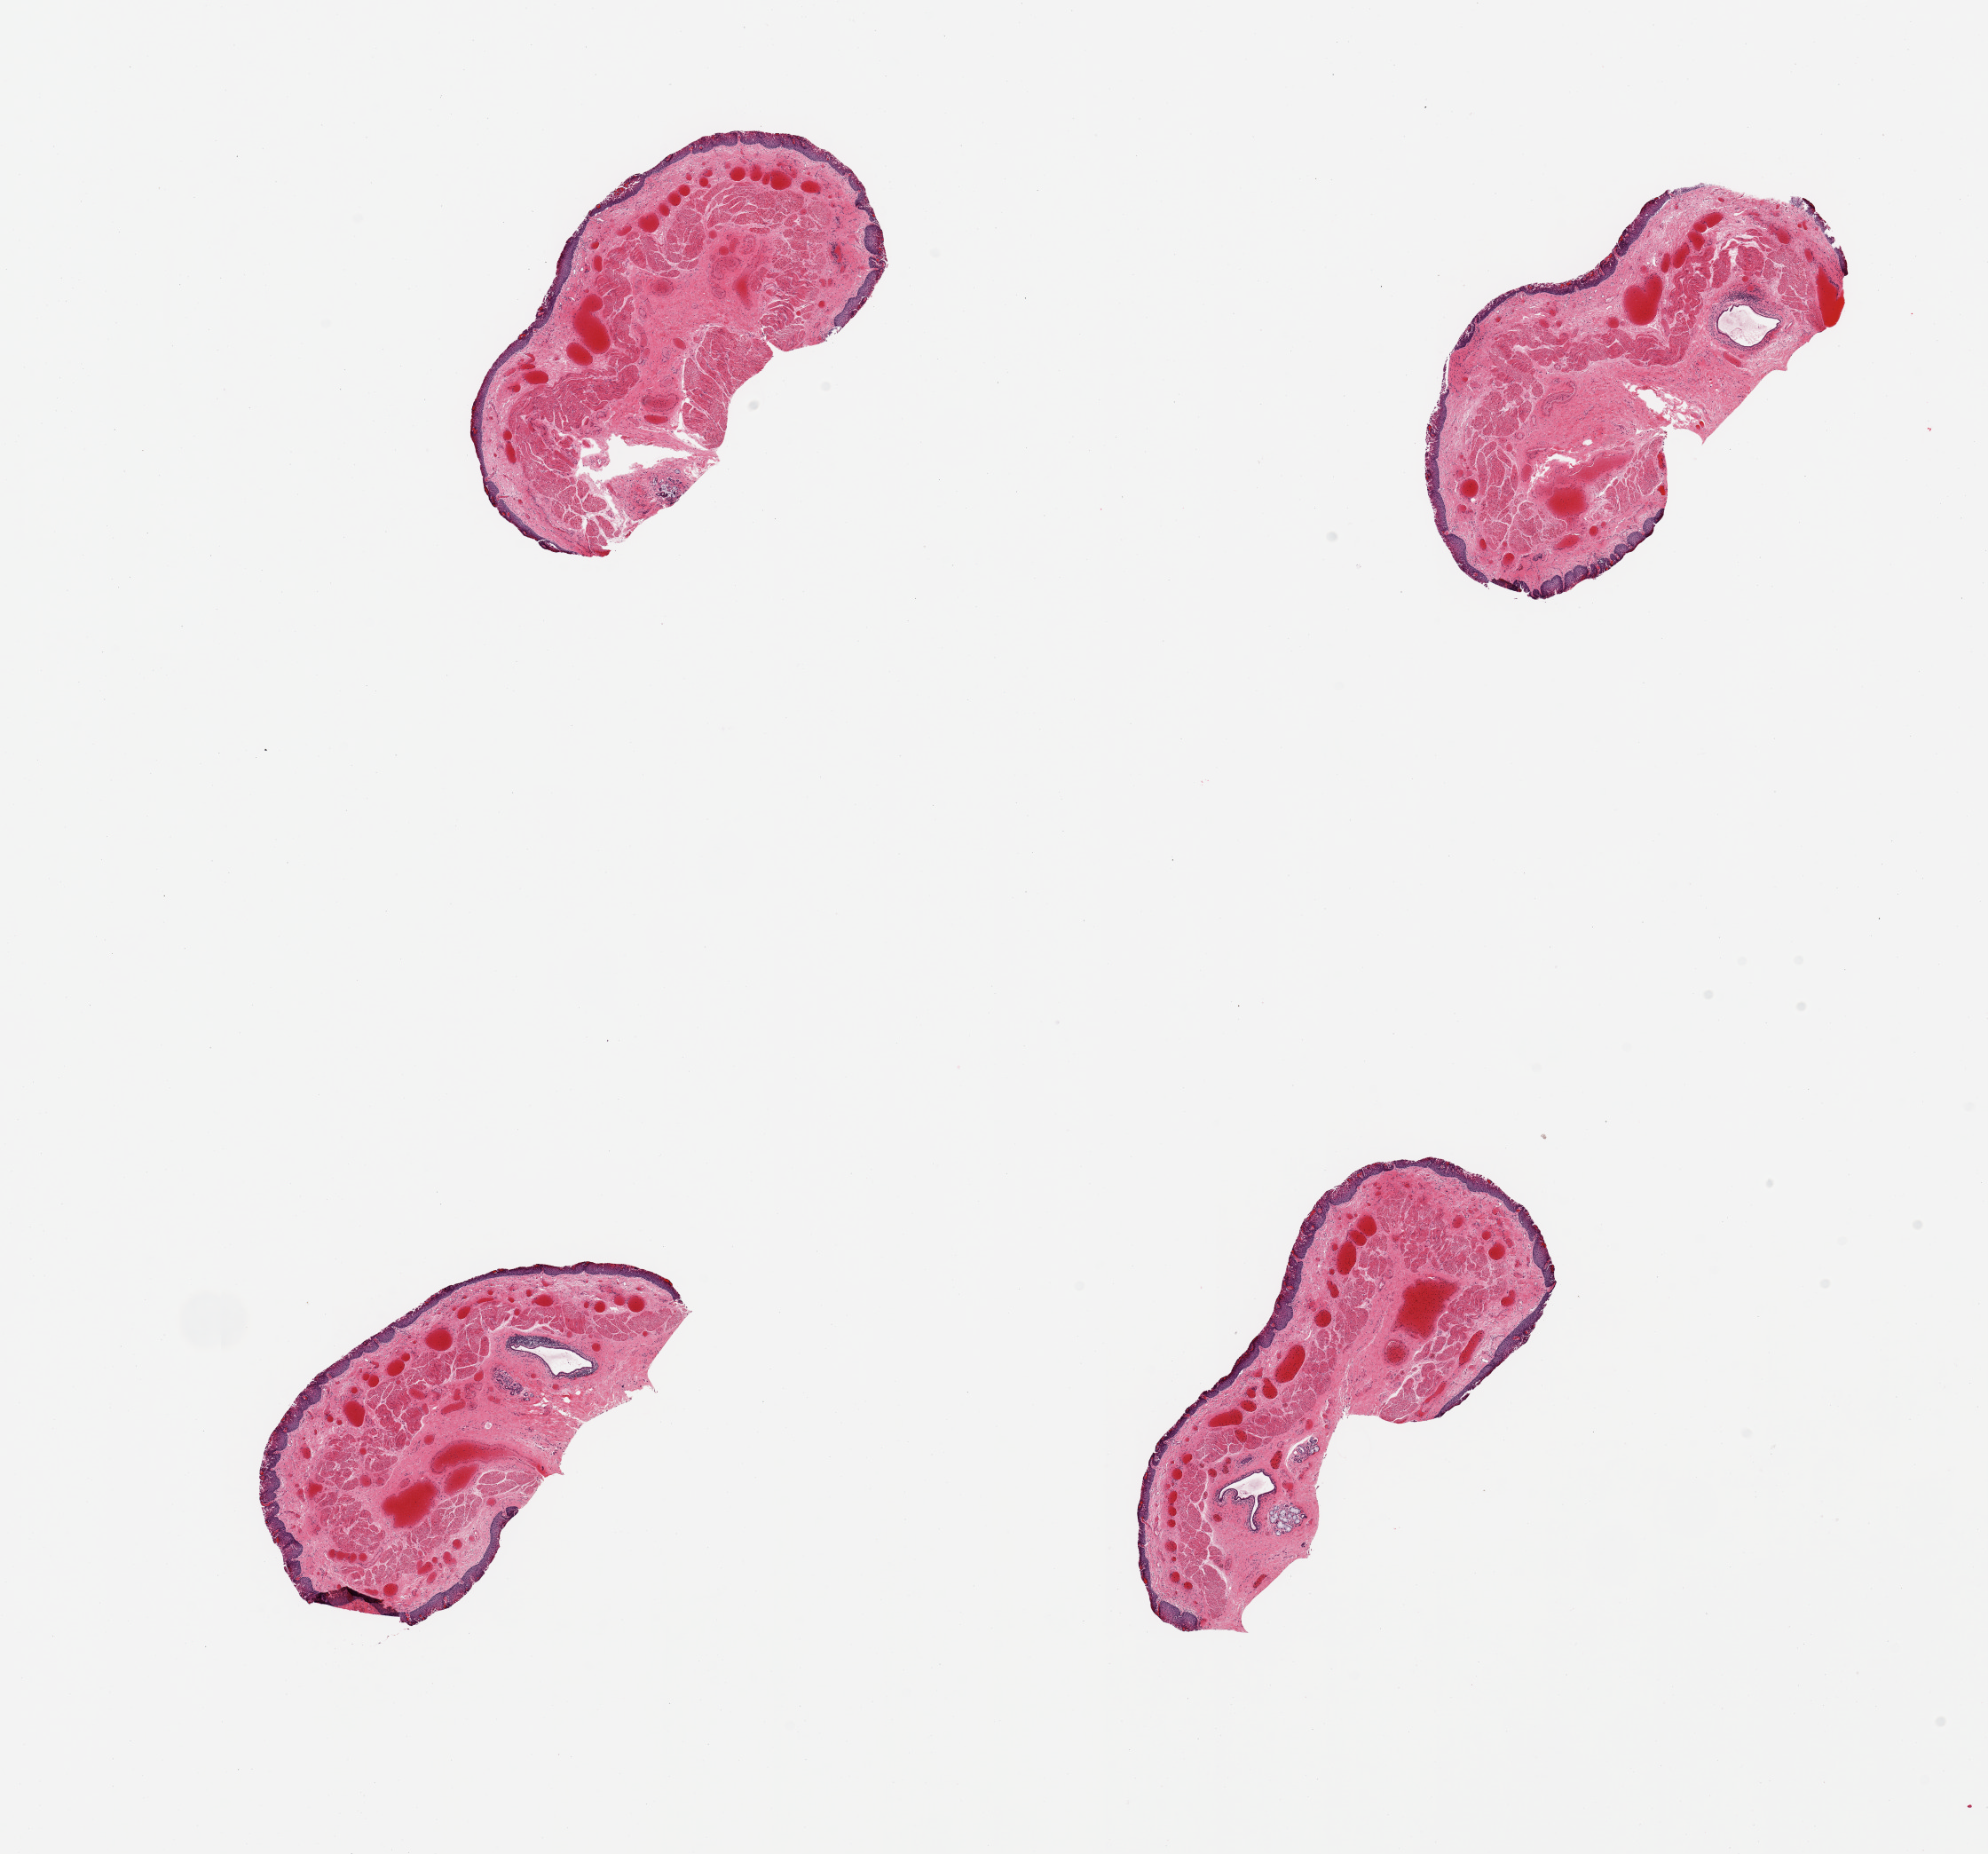
Digitized H&E-stained section — whole scanned area (about 17.7 x 16.5 mm) shown as a low-resolution overview; PAXgene-fixed paraffin-embedded (PFPE) section; sampled site (target tissue): esophageal mucous membrane; donor tissue sample. Donor sex: male.
Pathologist's review note for this sample: 4 pieces; surface sloughing; congestion.